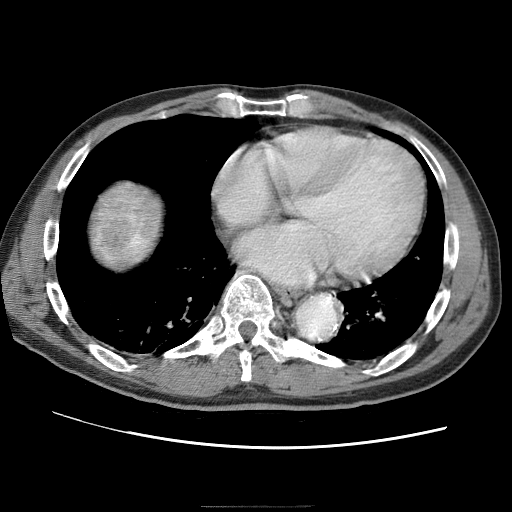
Contrast-enhanced abdominal CT (liver protocol), one axial slice. Position 70 of 75 along the scan axis. Reconstruction kernel STANDARD. One of 2 acquisitions stored at this slice position. Soft-tissue window (W 400 / L 40 HU). 512 × 512 image matrix, field of view 360 × 360 mm. From the clinical record (not read from this slice): diagnosis: hepatocellular carcinoma (patient treated with transarterial chemoembolisation; whether this scan precedes or follows treatment is not stated here); TNM stage (as recorded): Stage-II; Child-Pugh class: A; tumour differentiation: well differentiated; tumour nodularity: multinodular.
Structures marked on this image (semi-automatically segmented with operator editing):
- liver parenchyma outside the tumour (the mass and vessels are separate outlines, so this box may not span the whole liver): bounding box <80,170,180,284> (left, top, right, bottom; pixels)
- mass: <83,173,157,273>